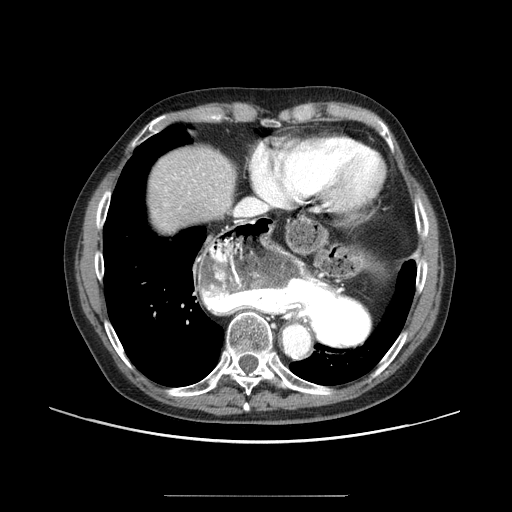
Contrast-enhanced abdominal CT (liver protocol), one axial slice; position 78 of 91 along the scan axis; 100 kVp; one of 2 acquisitions stored at this slice position; soft-tissue window (W 400 / L 40 HU); 2.5 mm slice thickness; 512 × 512 image matrix, field of view 400 × 400 mm. From the clinical record (not read from this slice): diagnosis: hepatocellular carcinoma (patient treated with transarterial chemoembolisation; whether this scan precedes or follows treatment is not stated here); TNM stage (as recorded): Stage-I; Child-Pugh class: A; tumour differentiation: moderately differentiated; tumour nodularity: uninodular.
Annotated regions visible in this slice (semi-automatically segmented with operator editing):
- abdominal aorta: box from (x=284, y=325) to (x=308, y=356) px
- liver parenchyma outside the tumour (the mass and vessels are separate outlines, so this box may not span the whole liver): (x=148, y=148)–(x=234, y=232)